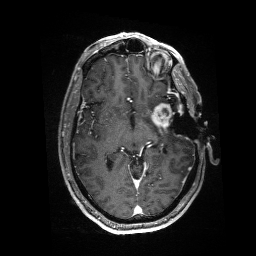
Brain MRI from a brain-tumour surgery series, one axial slice; slice 92 of 176 in the series (ordered by position); T1-weighted post-contrast; 1 mm slice thickness; 256 × 256 image matrix. Case-level facts recorded for this patient, not image findings: histopathology: Glioblastoma; WHO grade: 4; IDH mutation: no; tumour location: Left Anterior/Superior Temporal.
Structures marked on this image (outlined manually by an expert reader):
- residual tumour: bounding box (x1, y1, x2, y2) in pixels: (152, 103, 184, 130)